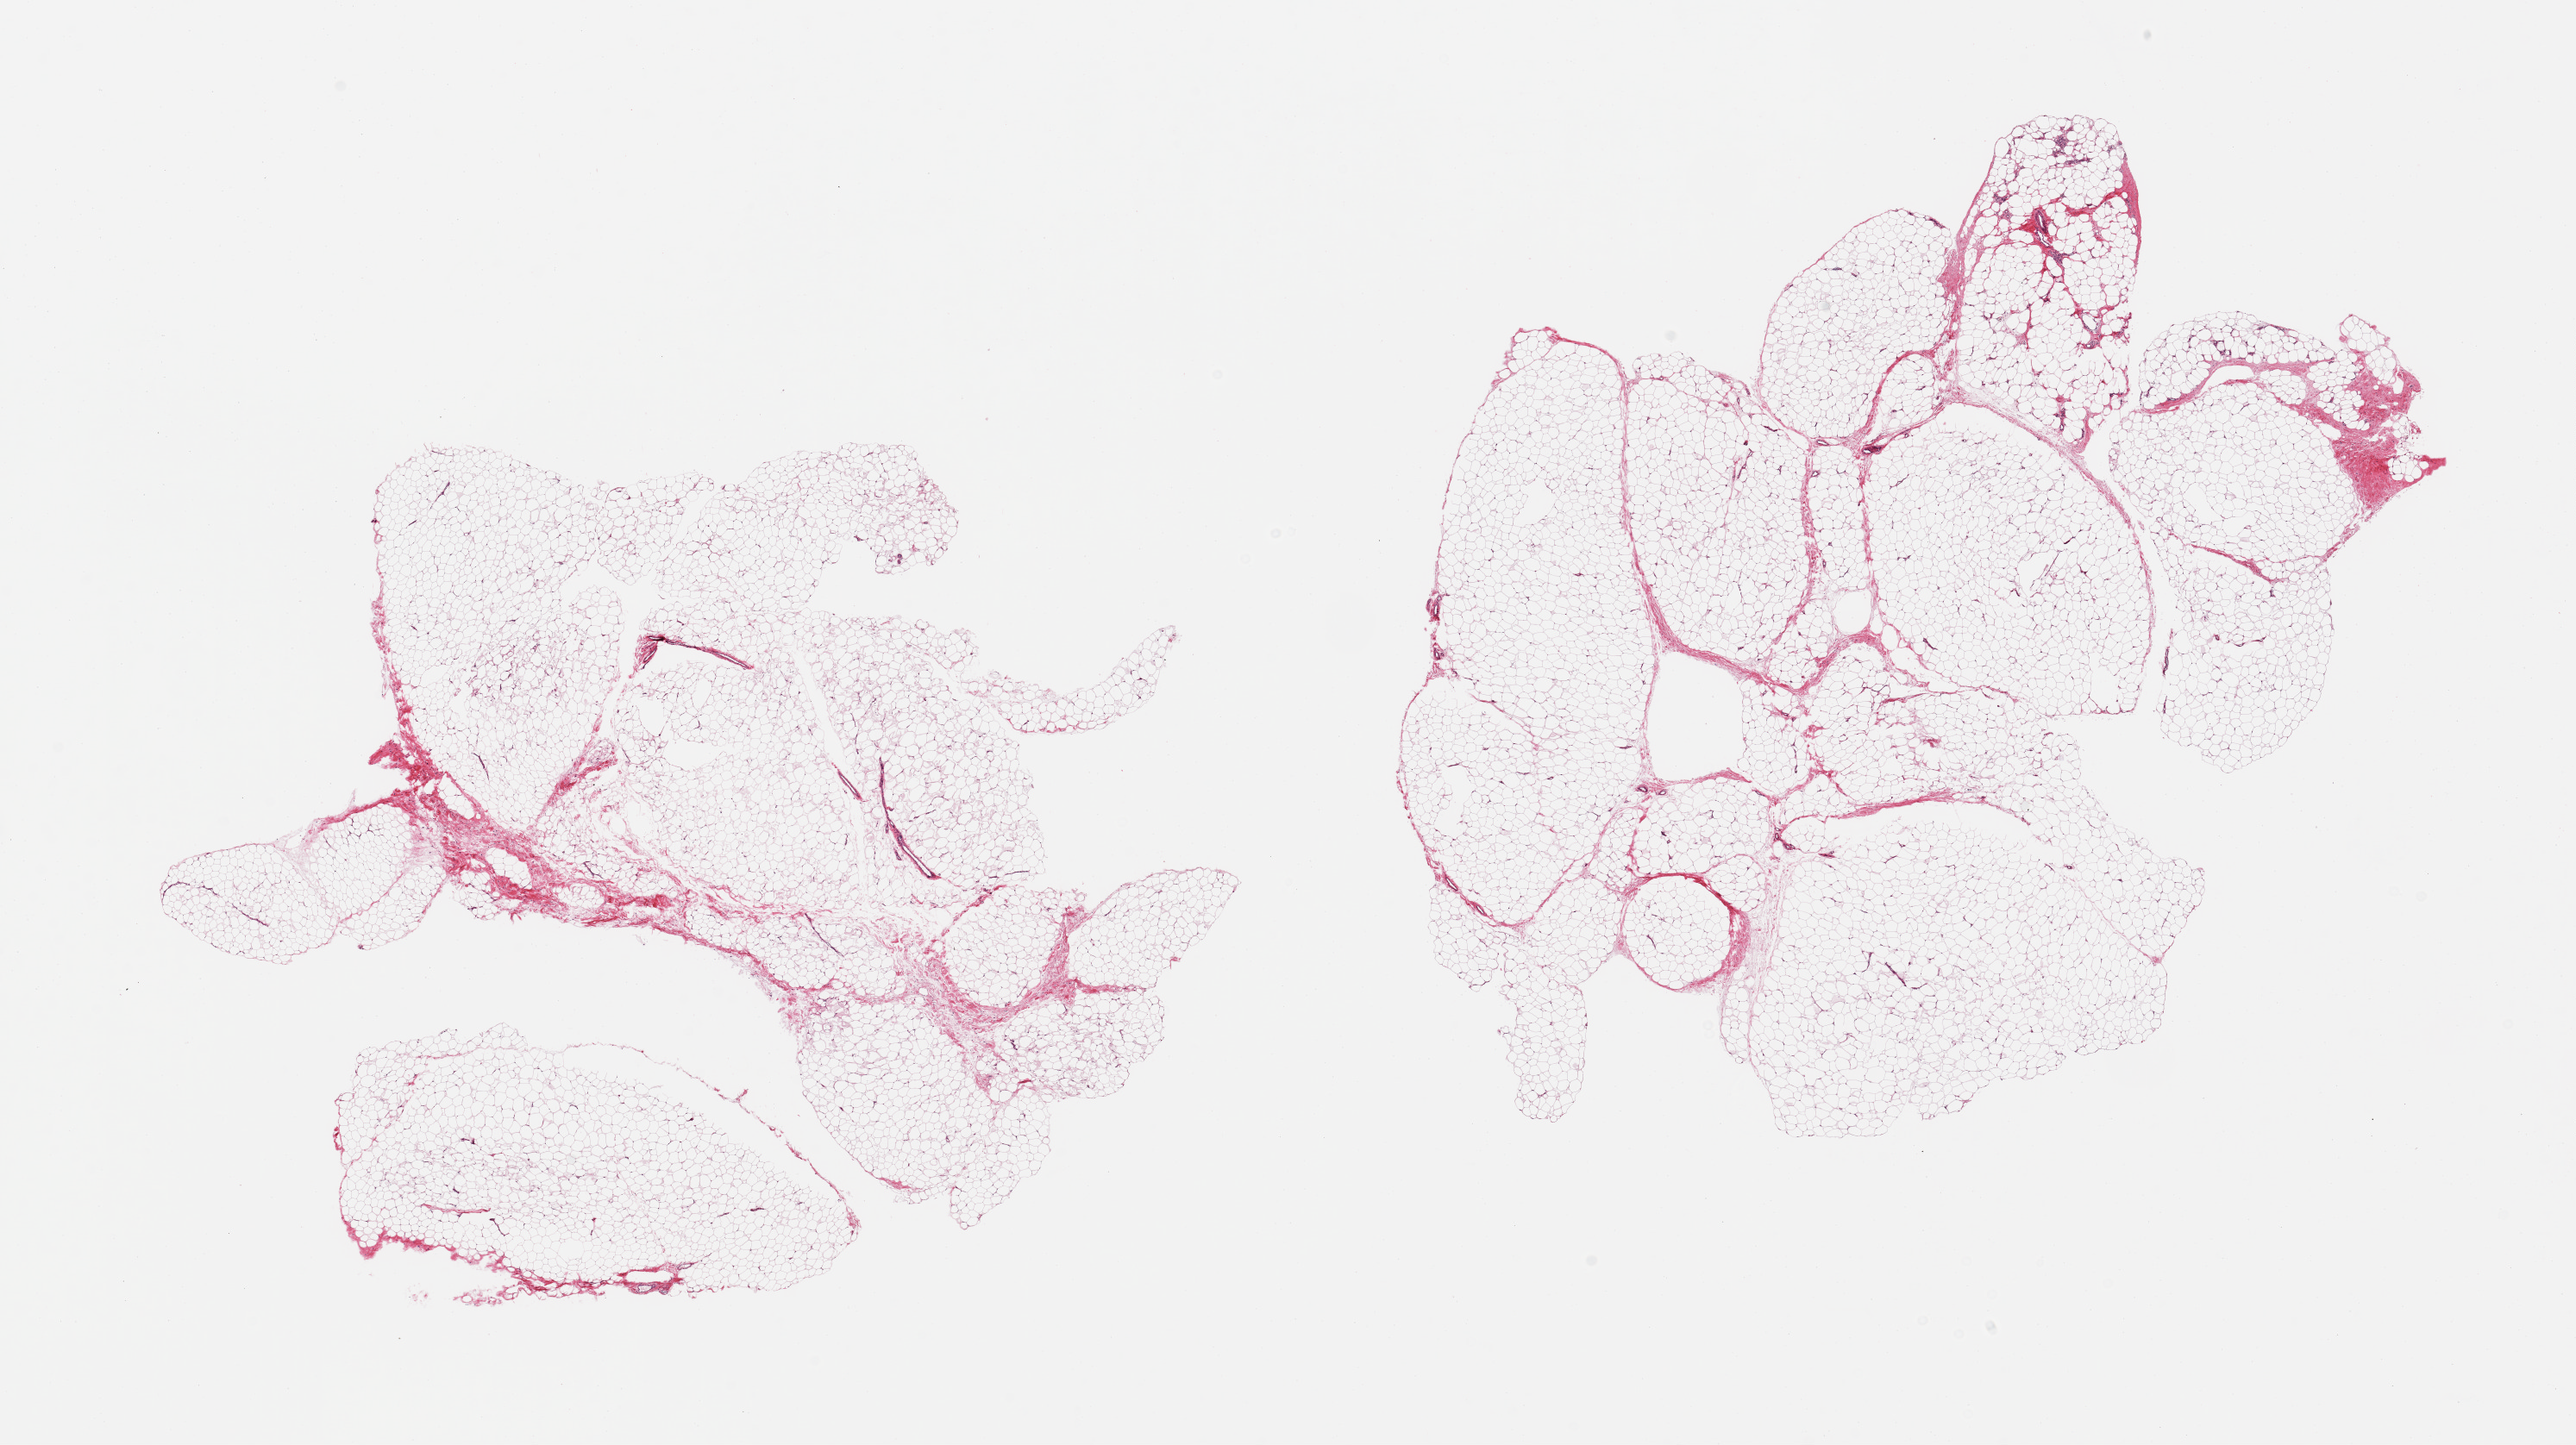
Whole-slide image, hematoxylin and eosin (H&E) stain — shown as a low-resolution overview of the whole scanned area (about 23.6 x 13.3 mm), PAXgene-fixed paraffin-embedded (PFPE) section, target tissue: adipose tissue, donor tissue sample. Female donor.
Reviewer comment on this tissue sample: 2 pieces; lobulated mature adipose tissue with thin fibrovascular septa.